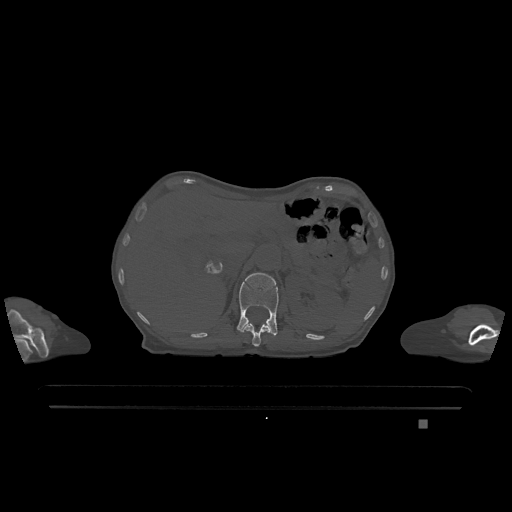
CT including the spine, one axial slice; position 495 of 1317 along the scan axis; bone window (W 1800 / L 400 HU); 0.5 mm slice thickness; 512 × 512 image matrix, field of view 500 × 500 mm. Patient: female, 74 years. From the clinical record (not read from this slice): primary cancer: lung; vertebrae with lytic lesions (as recorded): T1, T4, T5, T6, L4, L5.
Outlined on this slice (semi-automatically segmented with operator editing):
- L1 vertebra: bounding box <237,273,279,336> (left, top, right, bottom; pixels)
- T12 vertebra: <241,323,270,347>